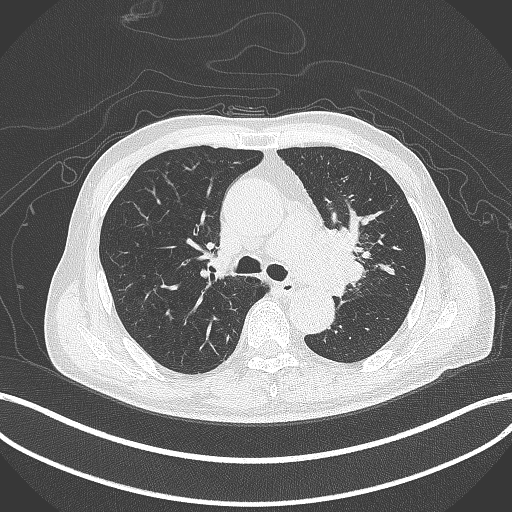
Chest CT, one axial slice. Slice 279 of 417 in the series (ordered by position). Reconstruction kernel B70f. 120 kVp. Lung window (W 1500 / L -600 HU). 1 mm slice thickness. 512 × 512 image matrix, field of view 400 × 400 mm. Male patient, age 77 years. Case-level facts recorded for this patient, not image findings: clinical TNM (as recorded): T3 N1 M0.
Annotated regions visible in this slice (bounding box drawn by a radiologist):
- lung tumour (recorded histology: adenocarcinoma): bounding box (x1, y1, x2, y2) in pixels: (314, 221, 375, 291)